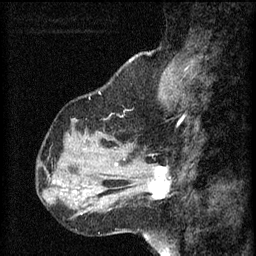
Breast MRI (dynamic contrast-enhanced), one sagittal slice; slice 18 of 60 in the series (ordered by position); 3 images stored at this slice position (order not interpretable as contrast timing); 1.5 T; TE 4.2 ms, TR 8.2 ms; 2 mm slice thickness; 256 × 256 image matrix. Female patient, age 37 years.
Annotated regions visible in this slice (semi-automatically segmented with operator editing):
- analysis volume of interest (the breast-tissue region the enhancement analysis was run in; not a lesion): box from (x=126, y=156) to (x=171, y=205) px
- tumour enhancement mask (voxels above the 70 % enhancement threshold inside the analysis volume of interest): (x=149, y=166)–(x=171, y=199)